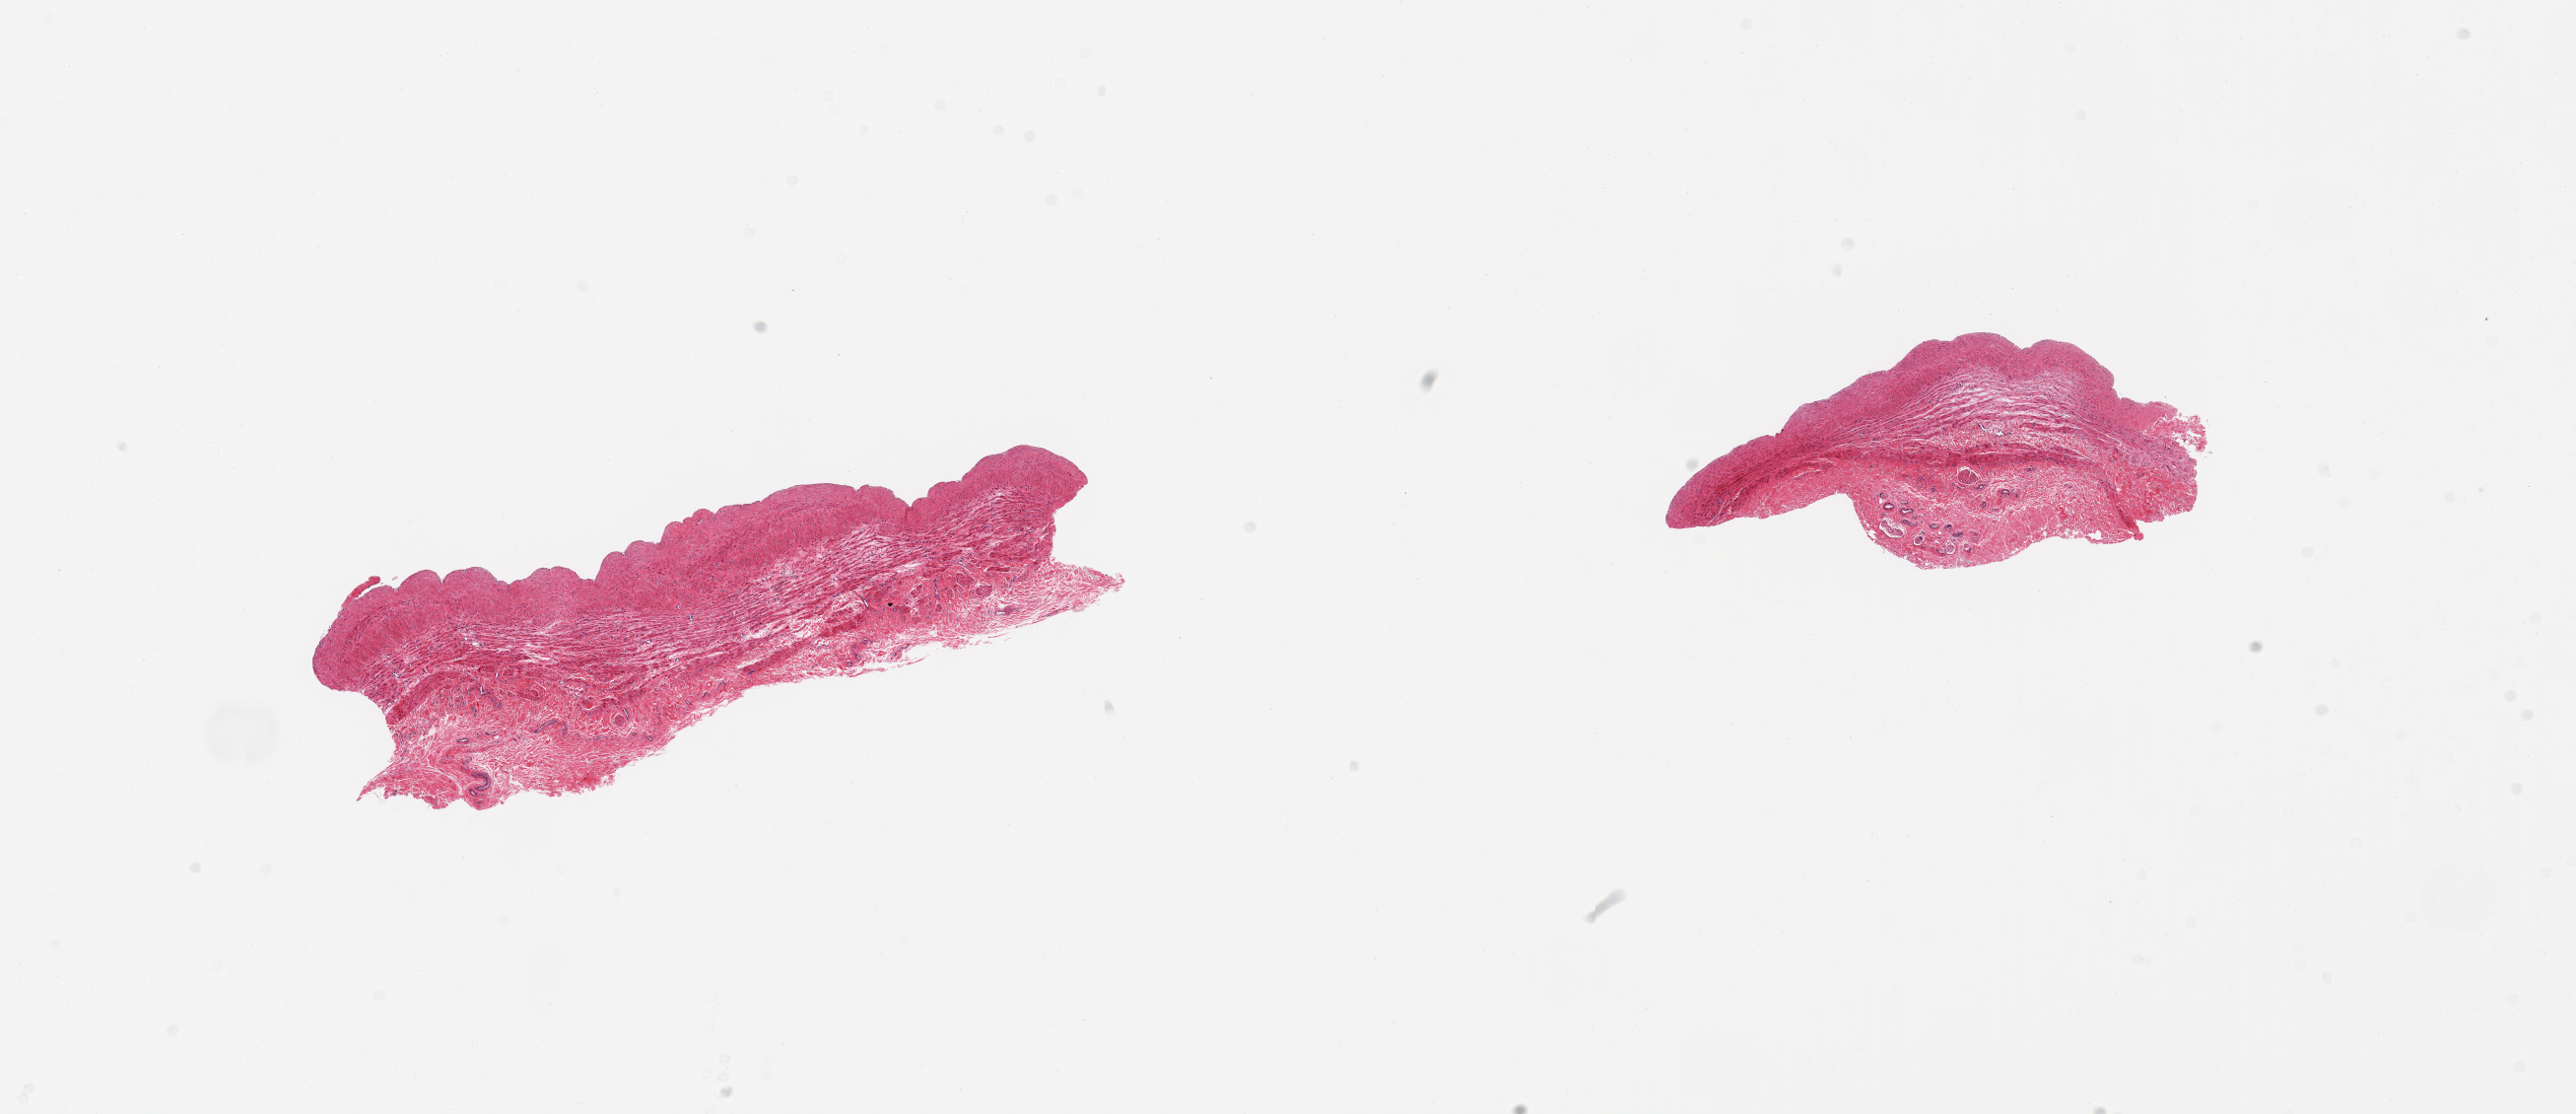
Whole-slide image, haematoxylin and eosin stain, a low-resolution overview of the entire scanned area, about 20.7 x 8.9 mm. PAXgene-fixed paraffin-embedded (PFPE) section. Section of tibial artery (target tissue). Donor tissue sample. Male donor.
Reviewer comment on this tissue sample: 2 pieces; portion of vessel wall.